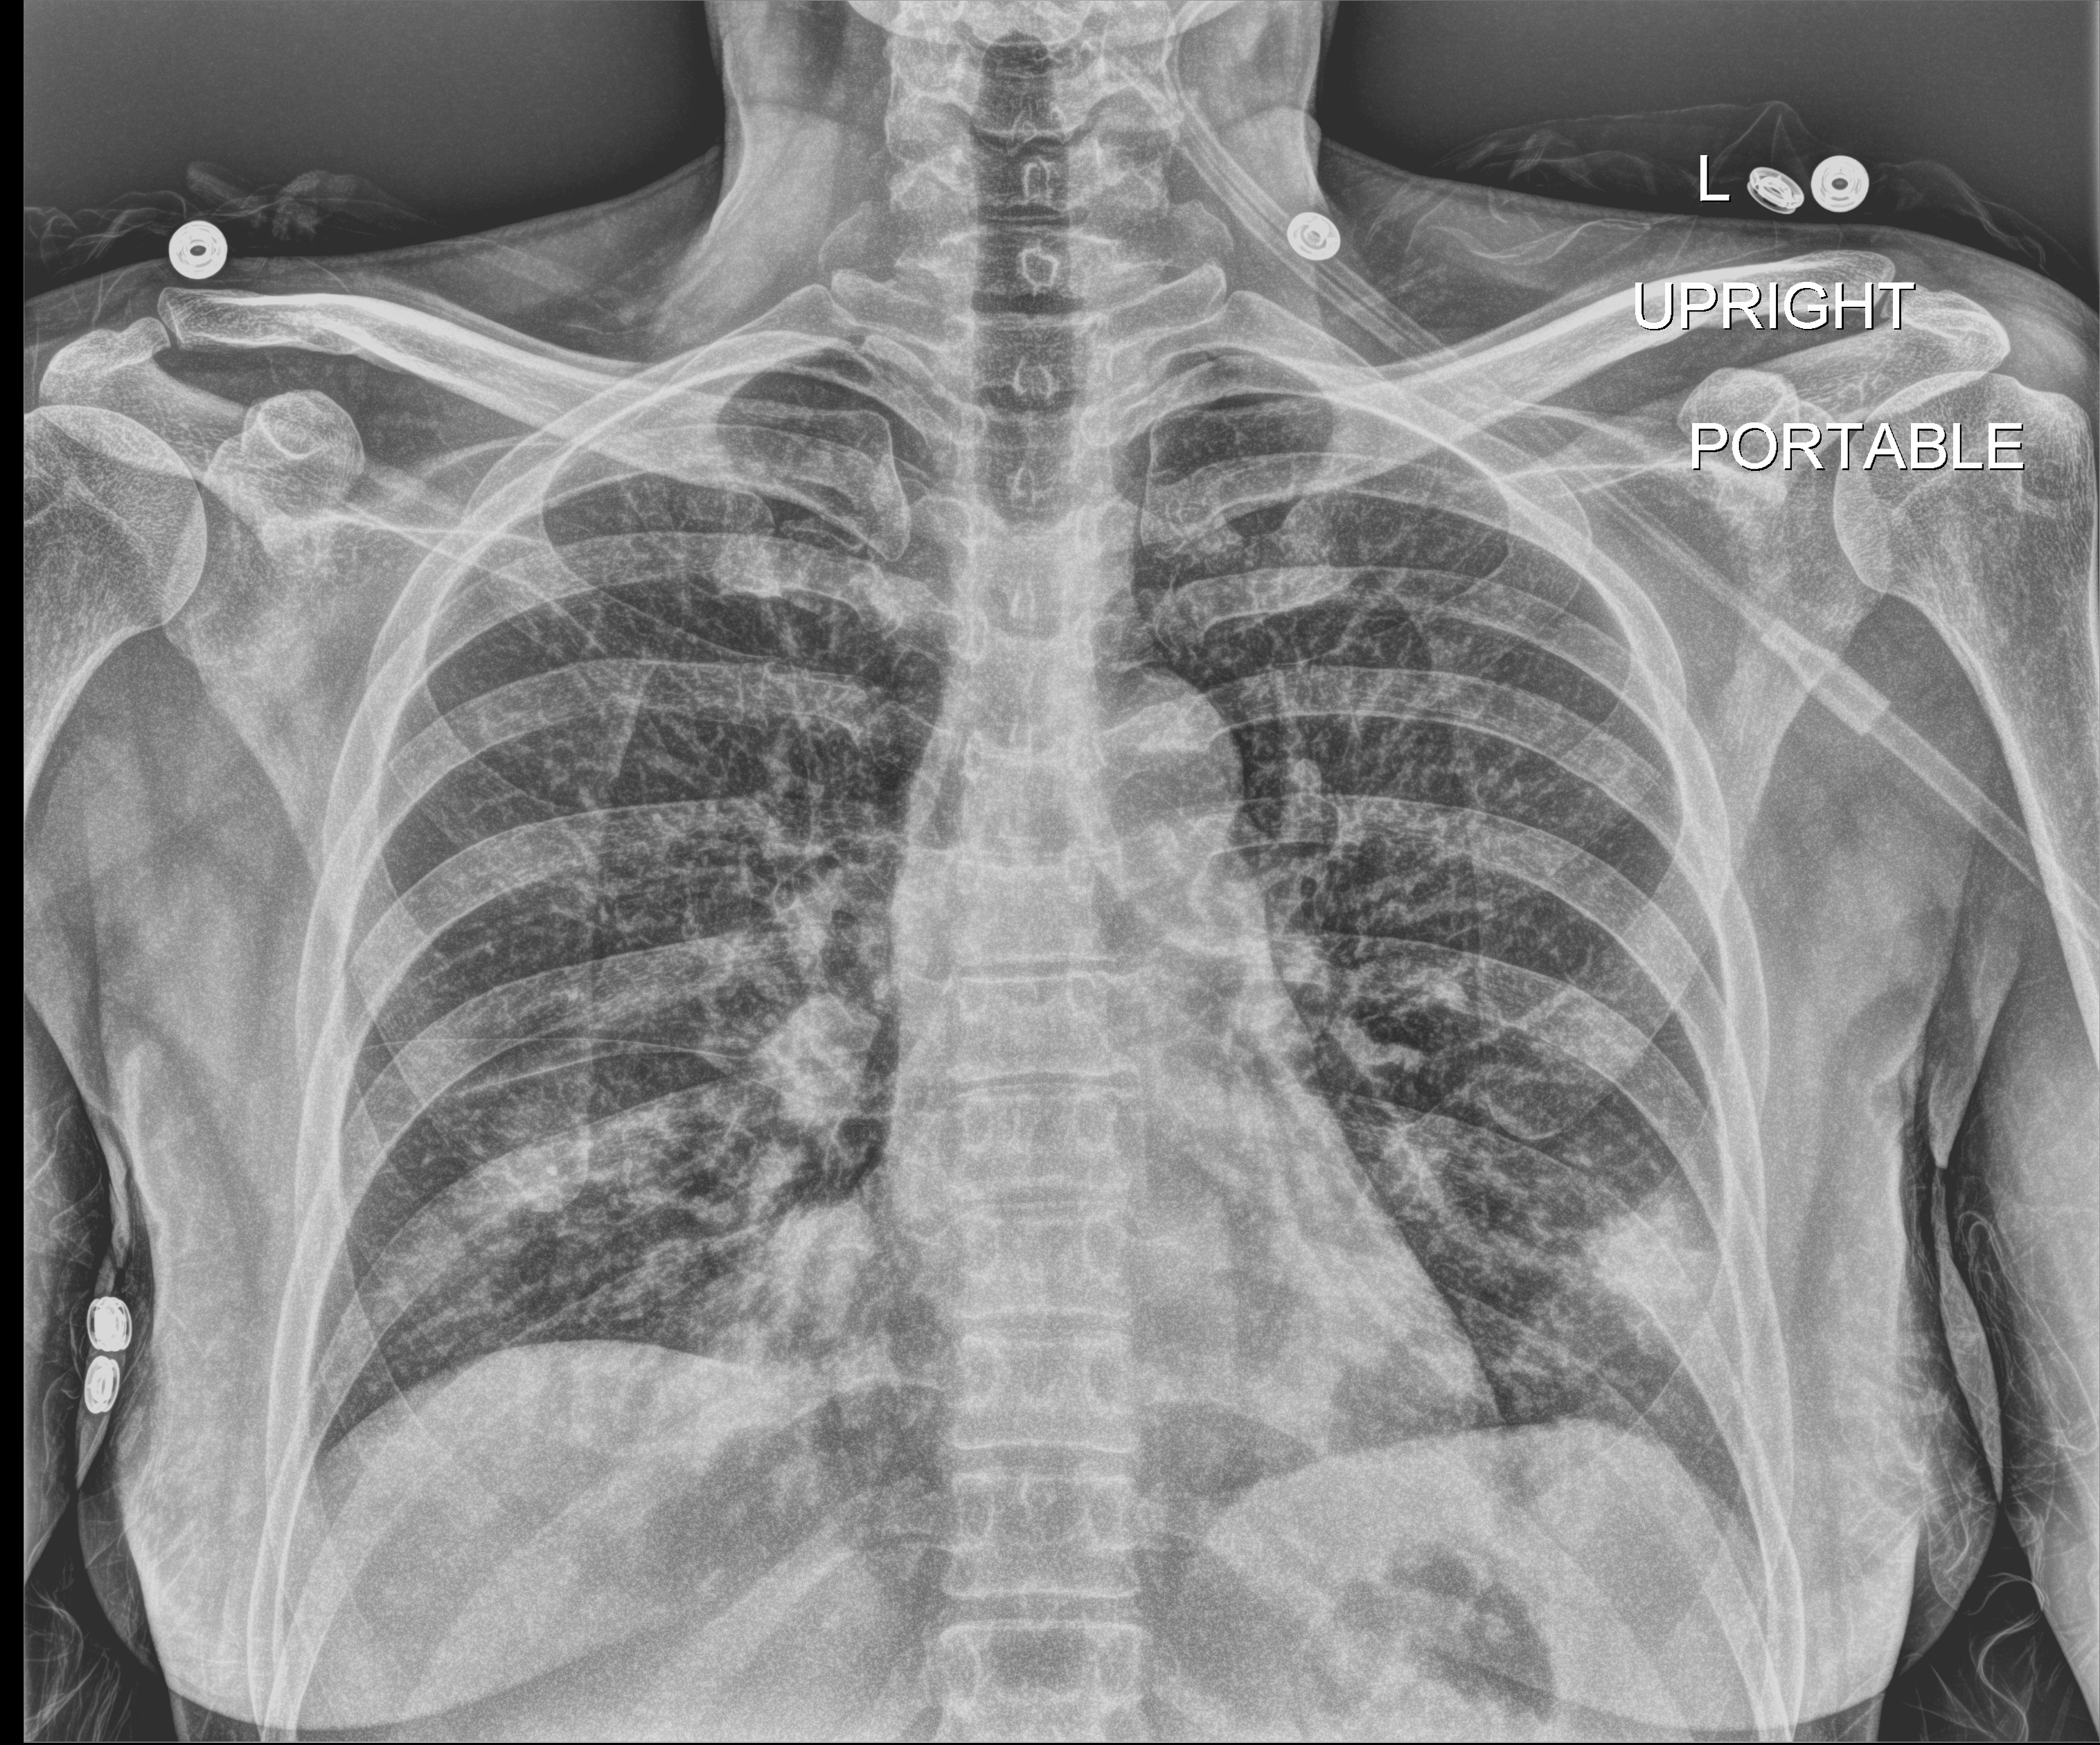
Chest X-ray (portable), anteroposterior (AP) projection. Patient hospitalised with COVID-19; female, aged 18–59 years.
From the hospital-stay record, not from the radiograph (when in the stay this image was taken is not recorded): admitted to intensive care during this hospital stay: yes.